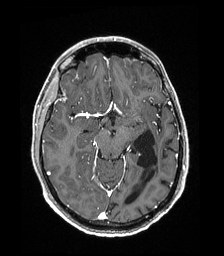
Brain MRI from a brain-tumour surgery series, one axial slice; position 109 of 192 along the scan axis; T1-weighted post-contrast; 224 × 256 image matrix. Case-level facts recorded for this patient, not image findings: histopathology: Low grade glioma; IDH mutation: no.
Structures marked on this image (manually delineated by an expert):
- previous resection cavity: box from (x=126, y=130) to (x=157, y=204) px